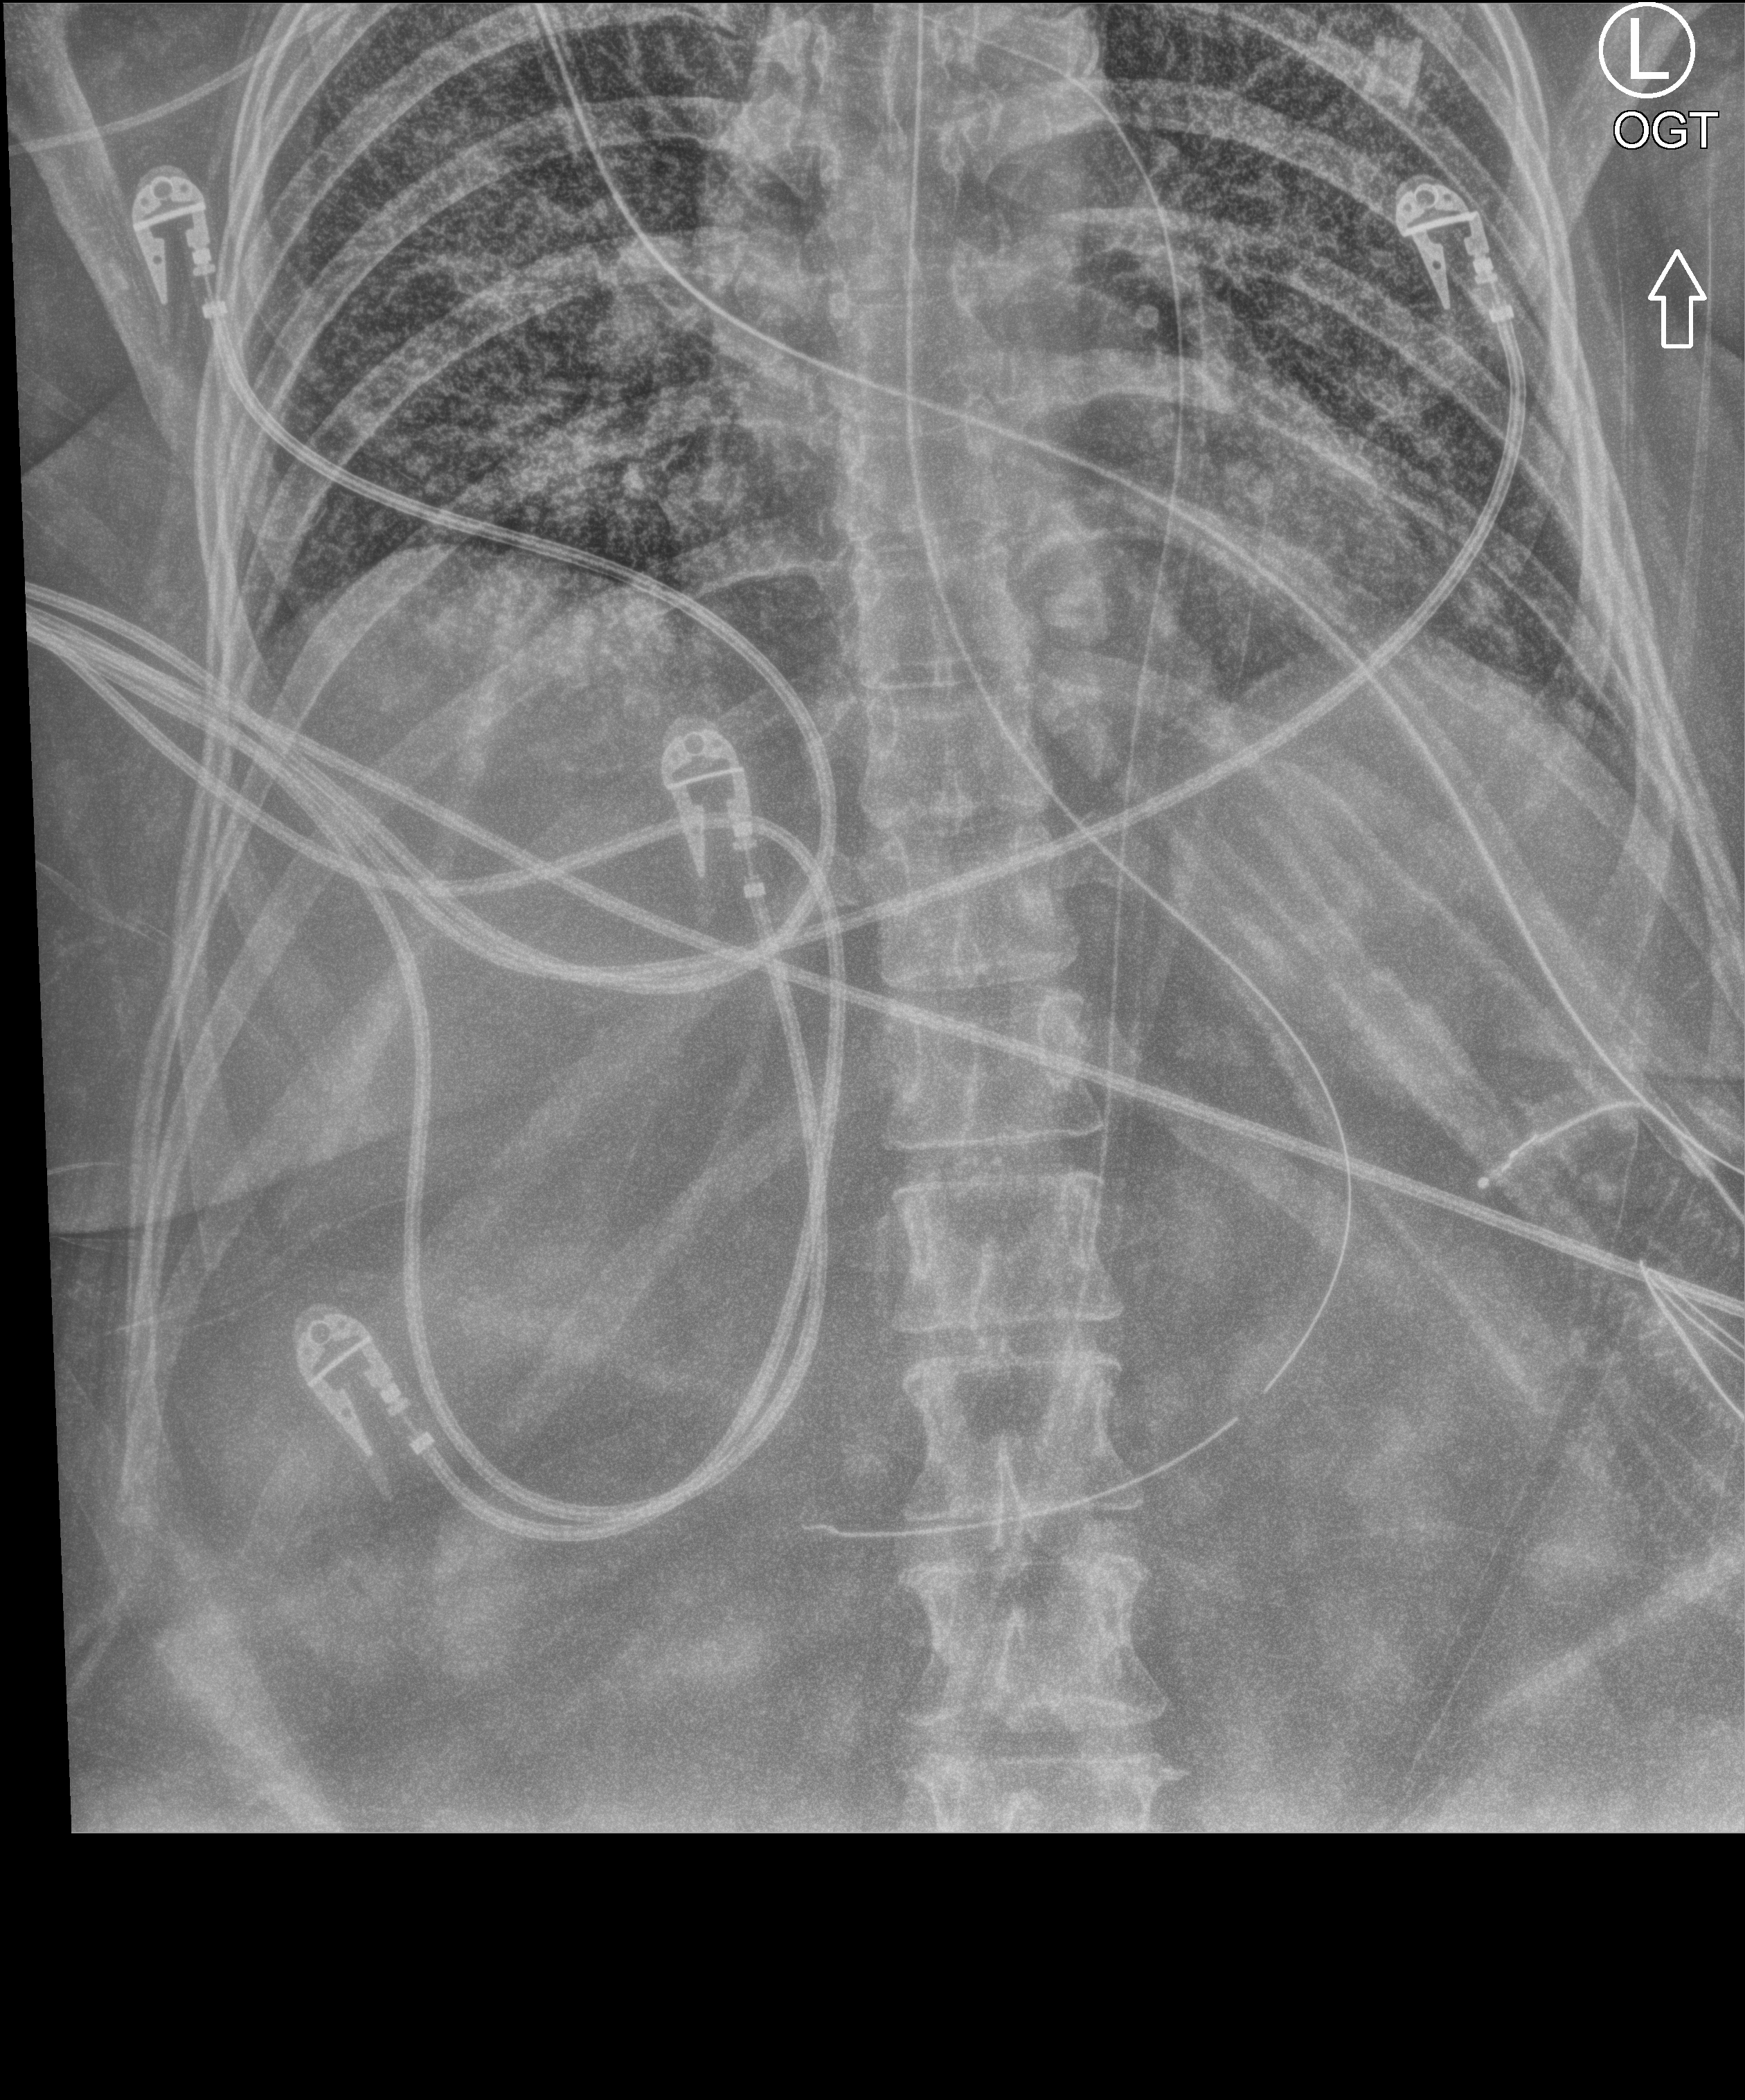
Bedside chest radiograph (computed radiography); anteroposterior (AP) projection. Patient hospitalised with COVID-19; female, aged 18–59 years.
Hospital-stay facts (about this admission, not read from this image; timing relative to this image not recorded): admitted to intensive care during this hospital stay: yes; mechanically ventilated during this hospital stay: yes; length of hospital stay: 73 days.